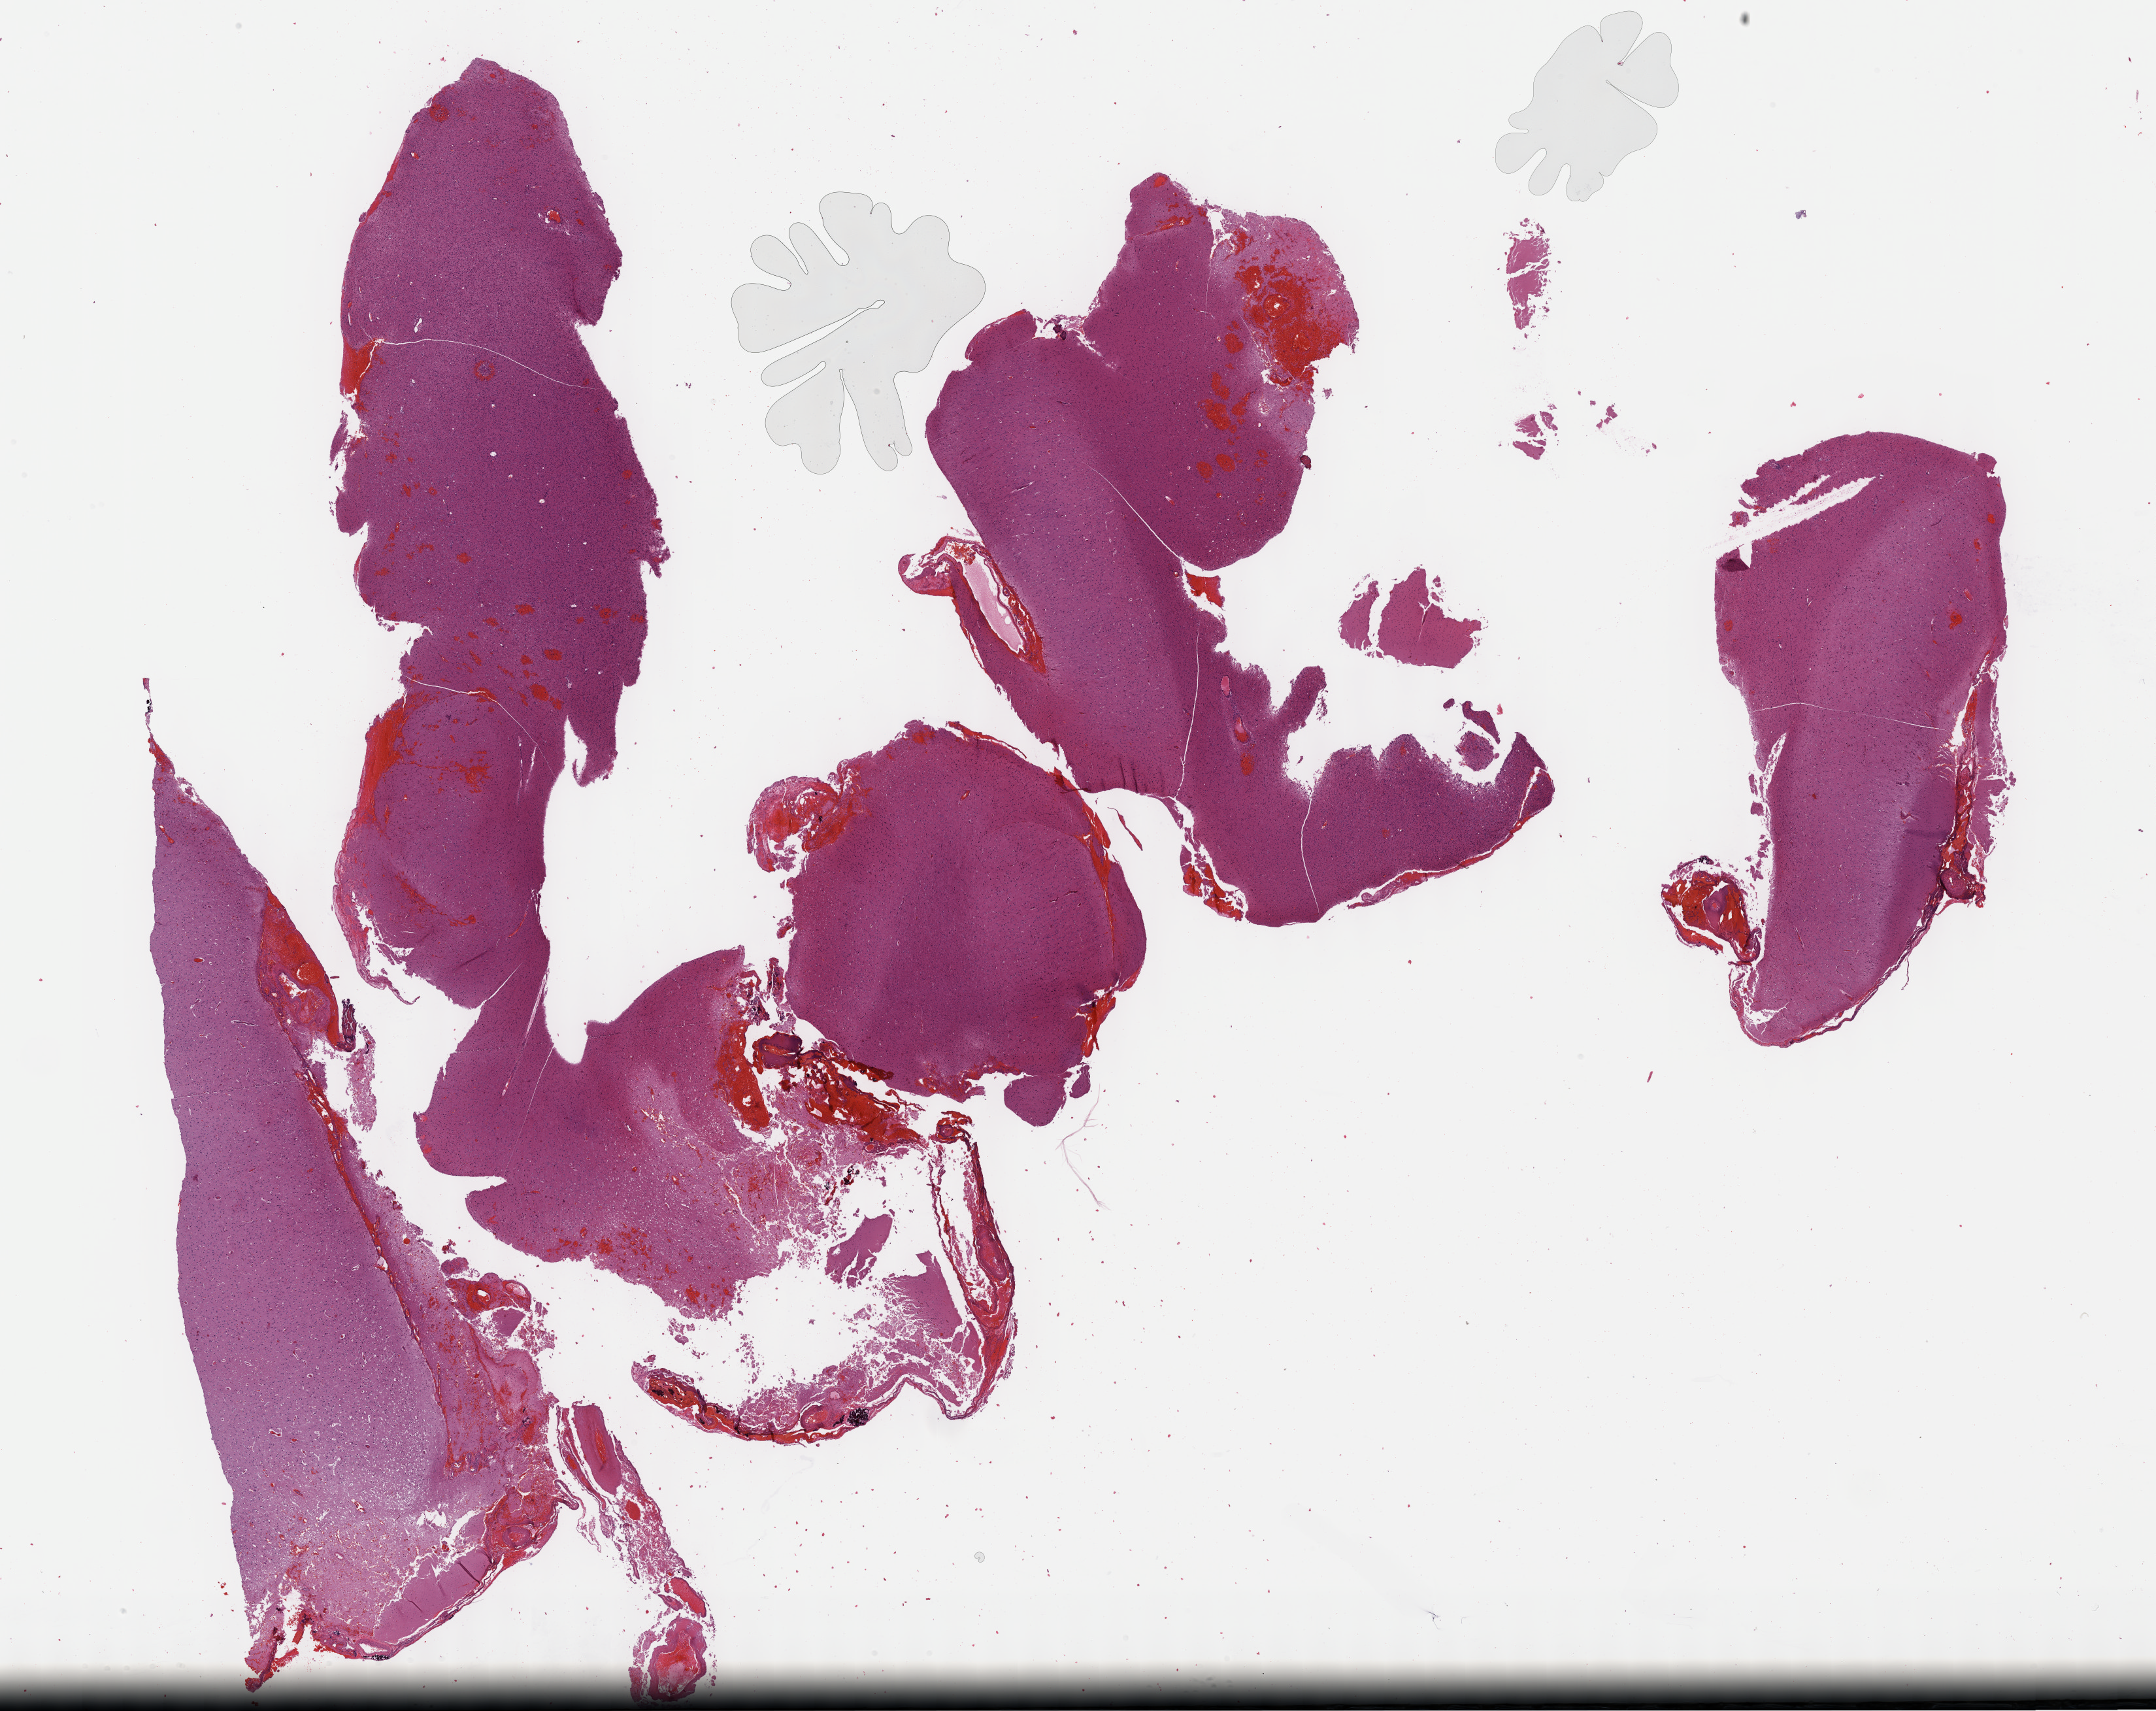
H&E-stained whole-slide image — shown as a low-resolution overview of the whole scanned area (about 26.7 x 21.2 mm, from a 40x scan), FFPE section, primary tumour sample from the brain. Female, age 30 years at initial diagnosis. Histologic grade: G2 (moderately differentiated).
• laterality: left
• diagnosis: Astrocytoma, NOS